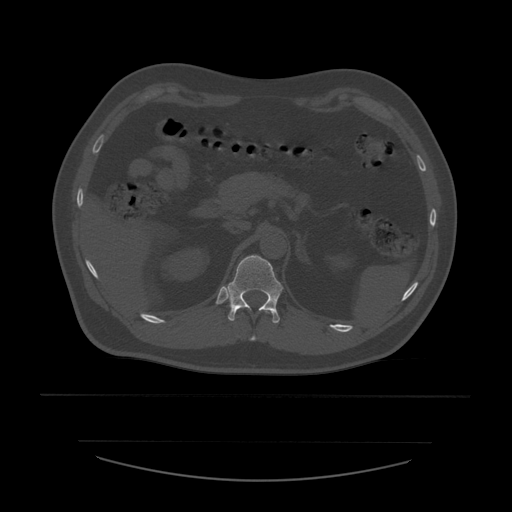
CT including the spine, one axial slice; position 257 of 532 along the scan axis; 120 kVp; bone window (W 1800 / L 400 HU); 1.25 mm slice thickness; 512 × 512 image matrix, field of view 441 × 441 mm. Patient age 44 years. Case-level facts recorded for this patient, not image findings: primary cancer: soft tissue sarcoma.
Structures marked on this image (semi-automatically segmented with operator editing):
- T11 vertebra: bounding box (x1, y1, x2, y2) in pixels: (235, 311, 270, 341)
- T12 vertebra: (225, 255, 283, 324)